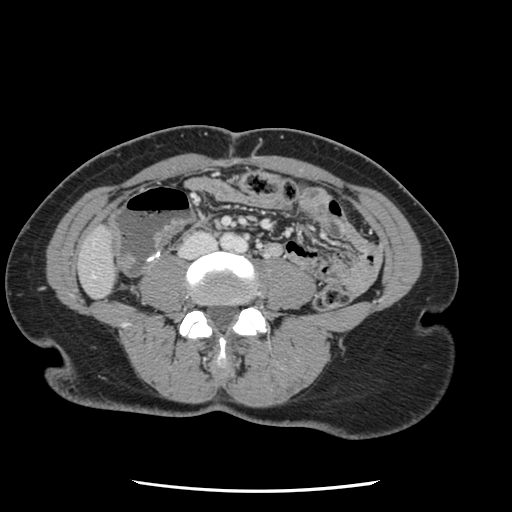
Contrast-enhanced abdominal CT, one axial slice. Position 2 of 134 along the scan axis. 120 kVp. Intravenous contrast given. Soft-tissue window (W 400 / L 40 HU). 512 × 512 image matrix, field of view 330 × 330 mm. Female patient, age 43 years. From the clinical record (not read from this slice): diagnosis: colorectal cancer liver metastases, imaged before liver resection; multiple liver metastases: yes; largest metastasis: 3.4 cm.
Annotated regions visible in this slice (expert manual segmentation):
- liver: box from (x=81, y=228) to (x=115, y=298) px
- planned liver remnant (the part of the liver to remain after resection): (x=81, y=229)–(x=115, y=298)